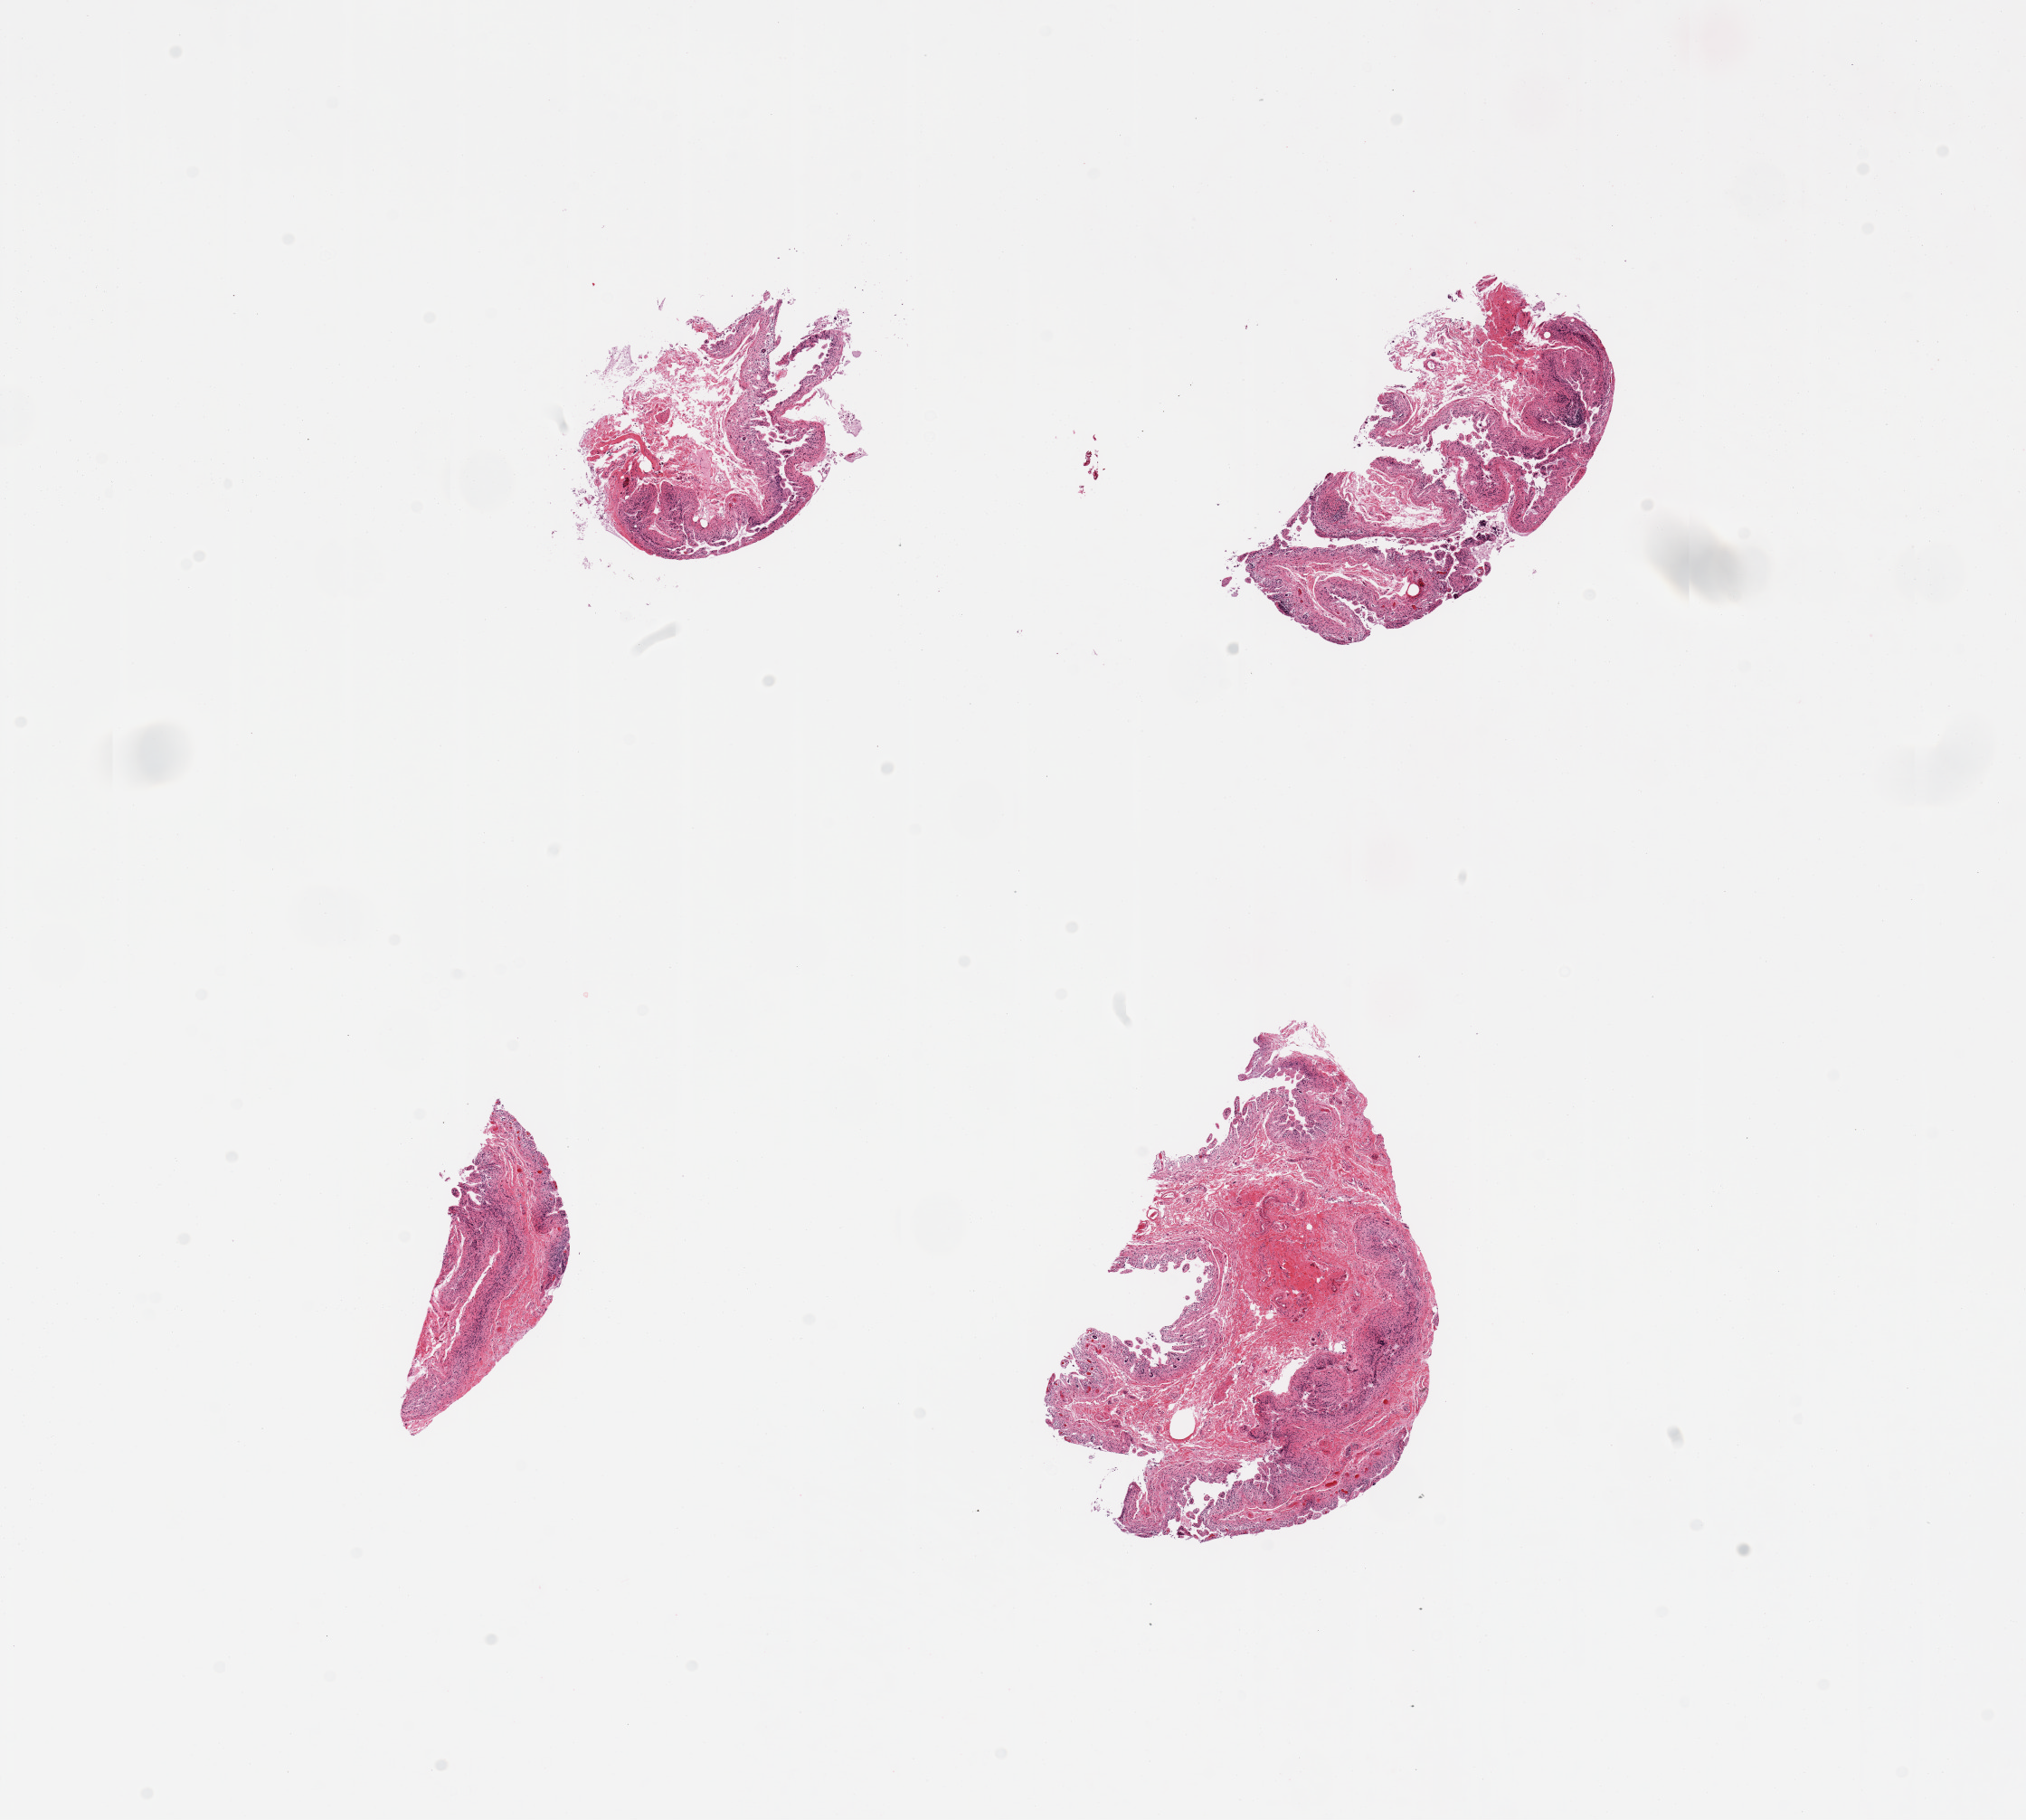
Haematoxylin and eosin whole-slide image — low-resolution overview of the scanned area, about 17.7 x 15.9 mm; PAXgene-fixed paraffin-embedded (PFPE) section; target tissue: ileum; tissue donor sample.
- pathologist's review note for this sample: 4 pieces; too little lymphoid tissue; excessive autolysis